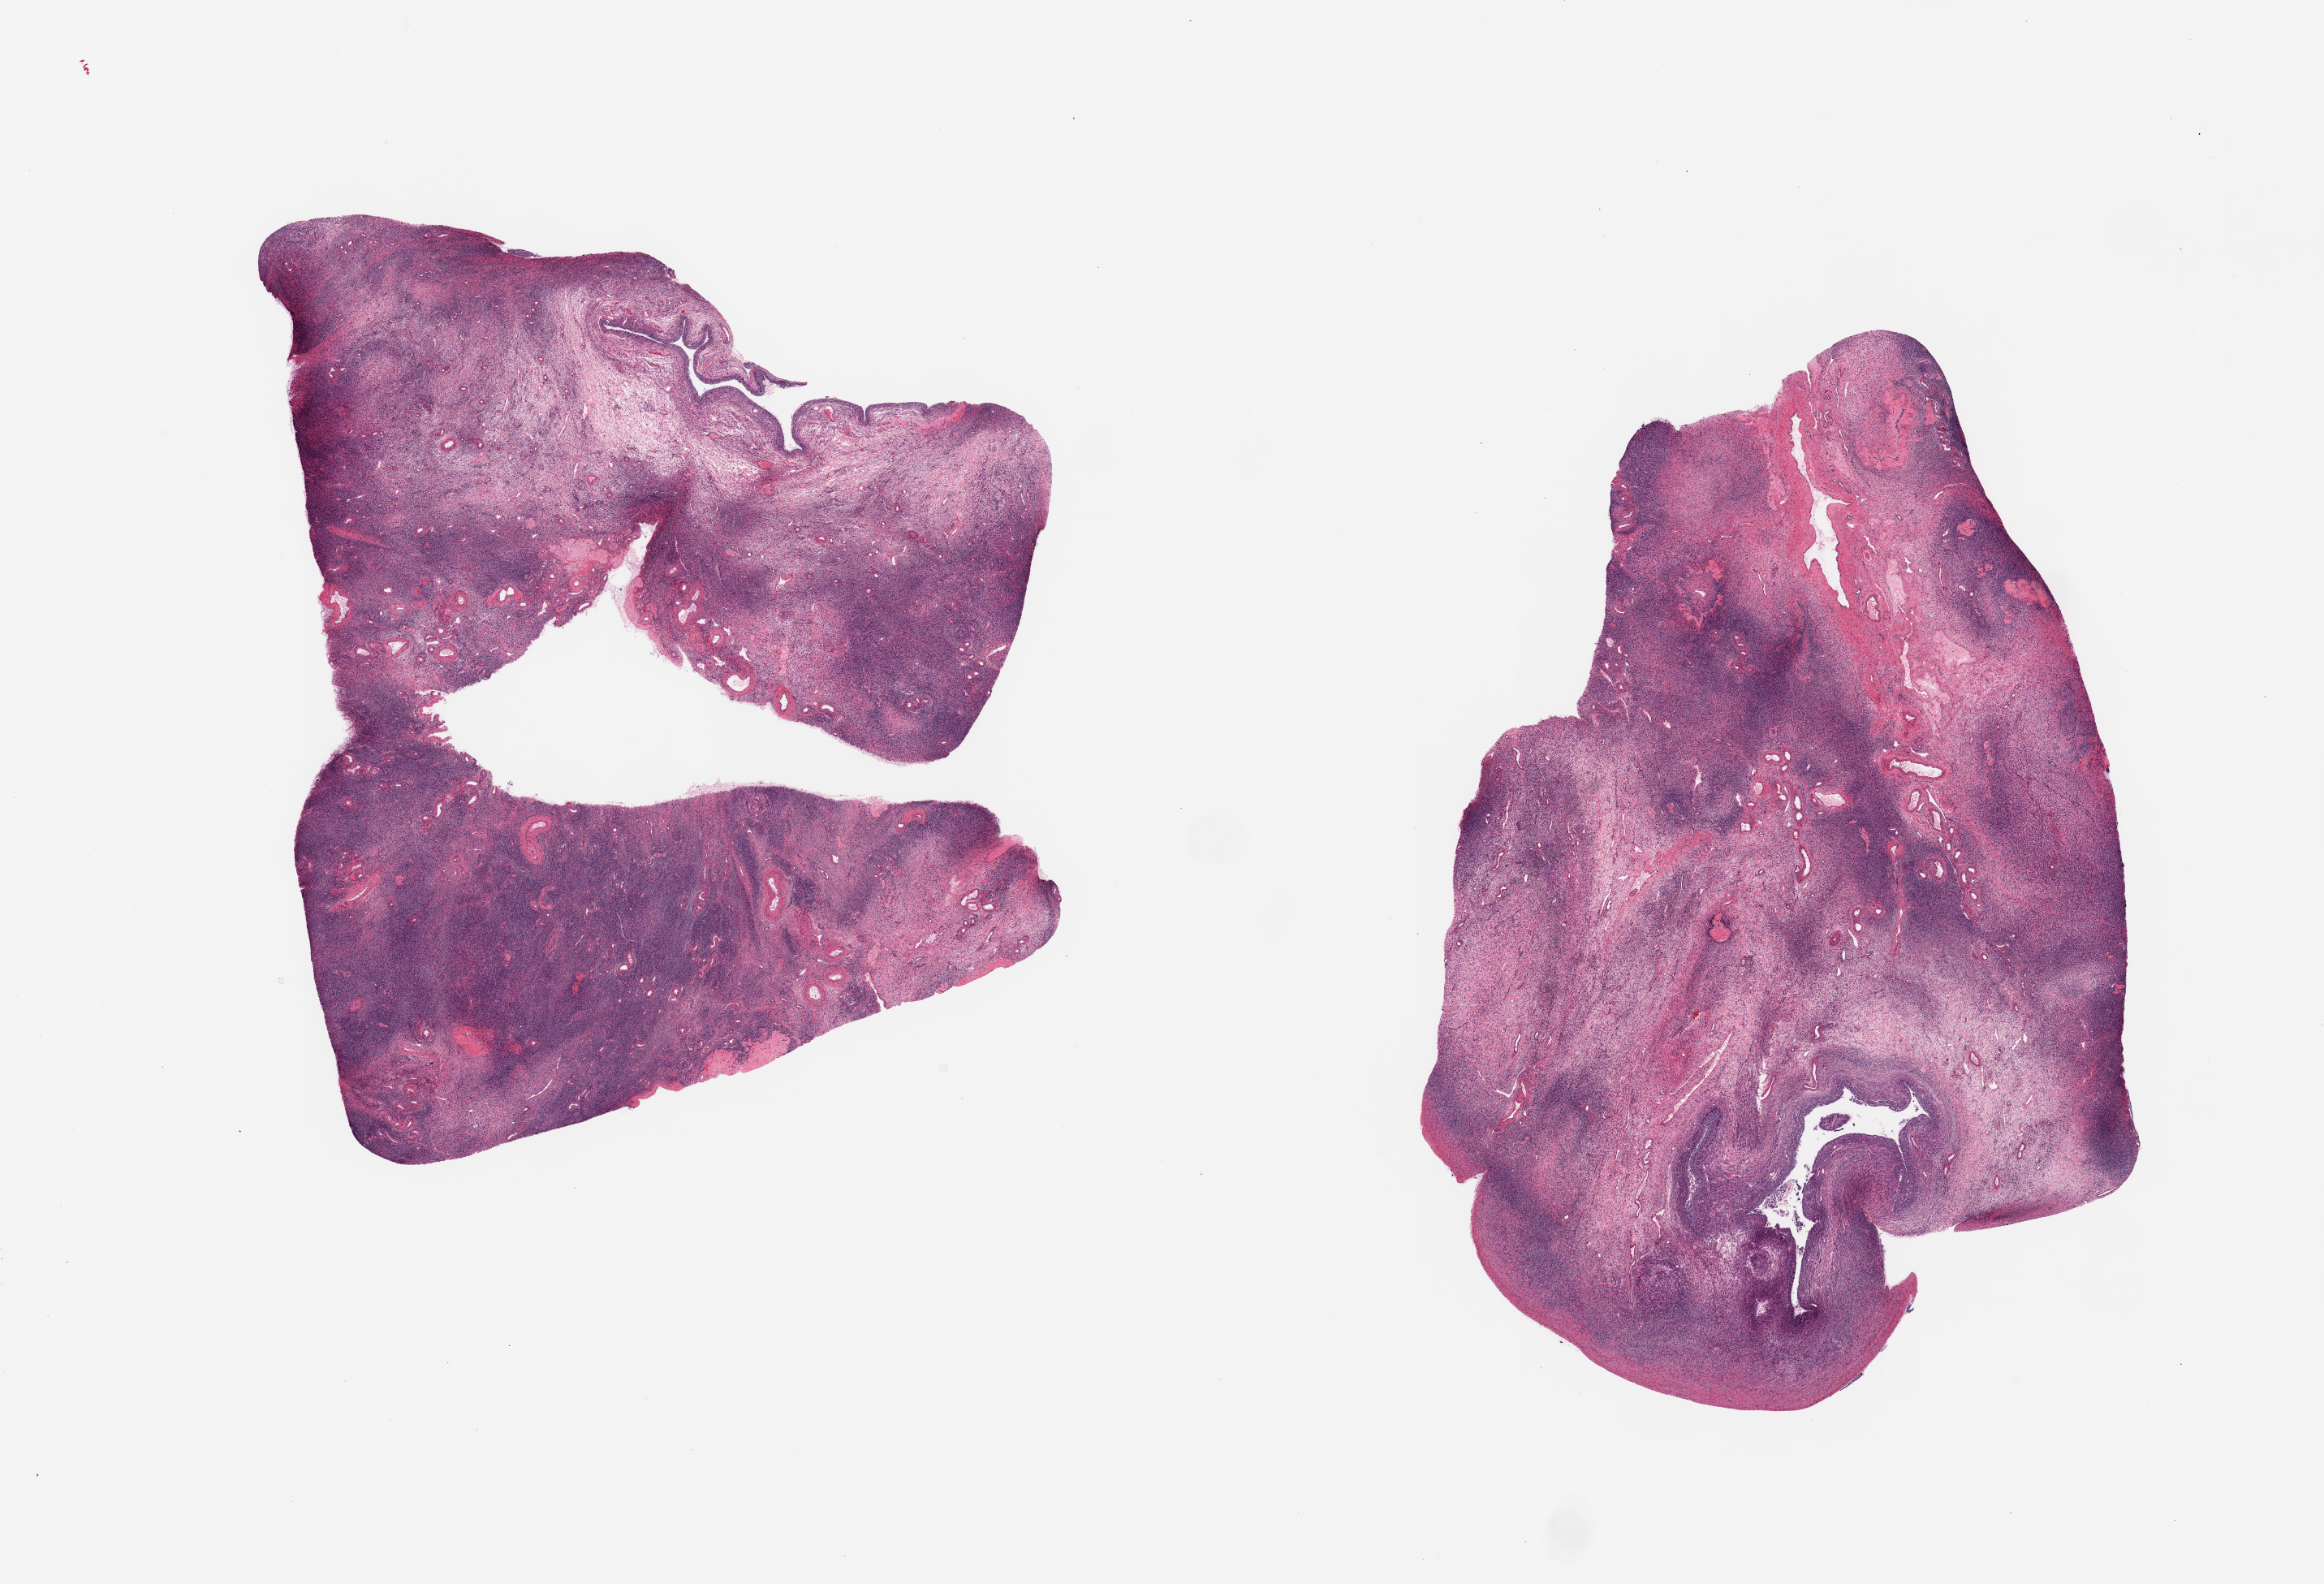
Whole-slide image, haematoxylin and eosin stain, brightfield — whole scanned area (about 22.6 x 15.4 mm) shown as a low-resolution overview. PAXgene-fixed paraffin-embedded (PFPE) section. Sampled site (target tissue): ovary. Tissue donor sample. Donor sex: female.
Reviewer comment on this tissue sample: 2 pieces, atrophic cortex for age, no abnormalities.